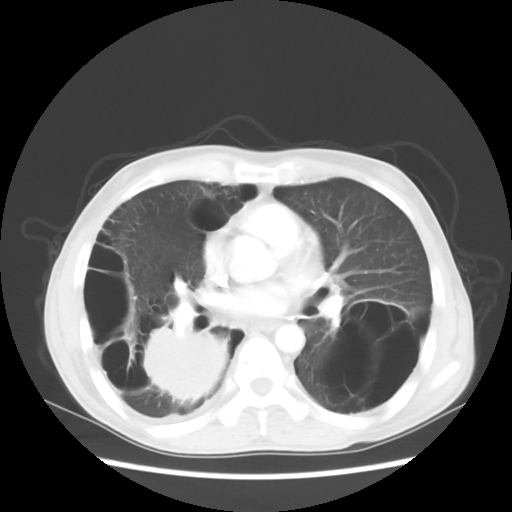
Chest CT, one axial slice; slice 27 of 56 in the series (ordered by position); 140 kVp; lung window (W 1500 / L -600 HU); 5 mm slice thickness; 512 × 512 image matrix. Male patient, age 41 years. Case-level facts recorded for this patient, not image findings: clinical TNM (as recorded): T4 N0 M1a; histopathological grade: G3.
Outlined on this slice (rectangle marked by the reading radiologist):
- lung tumour (recorded histology: large cell carcinoma): bounding box [x1, y1, x2, y2] px = [132, 326, 242, 415]